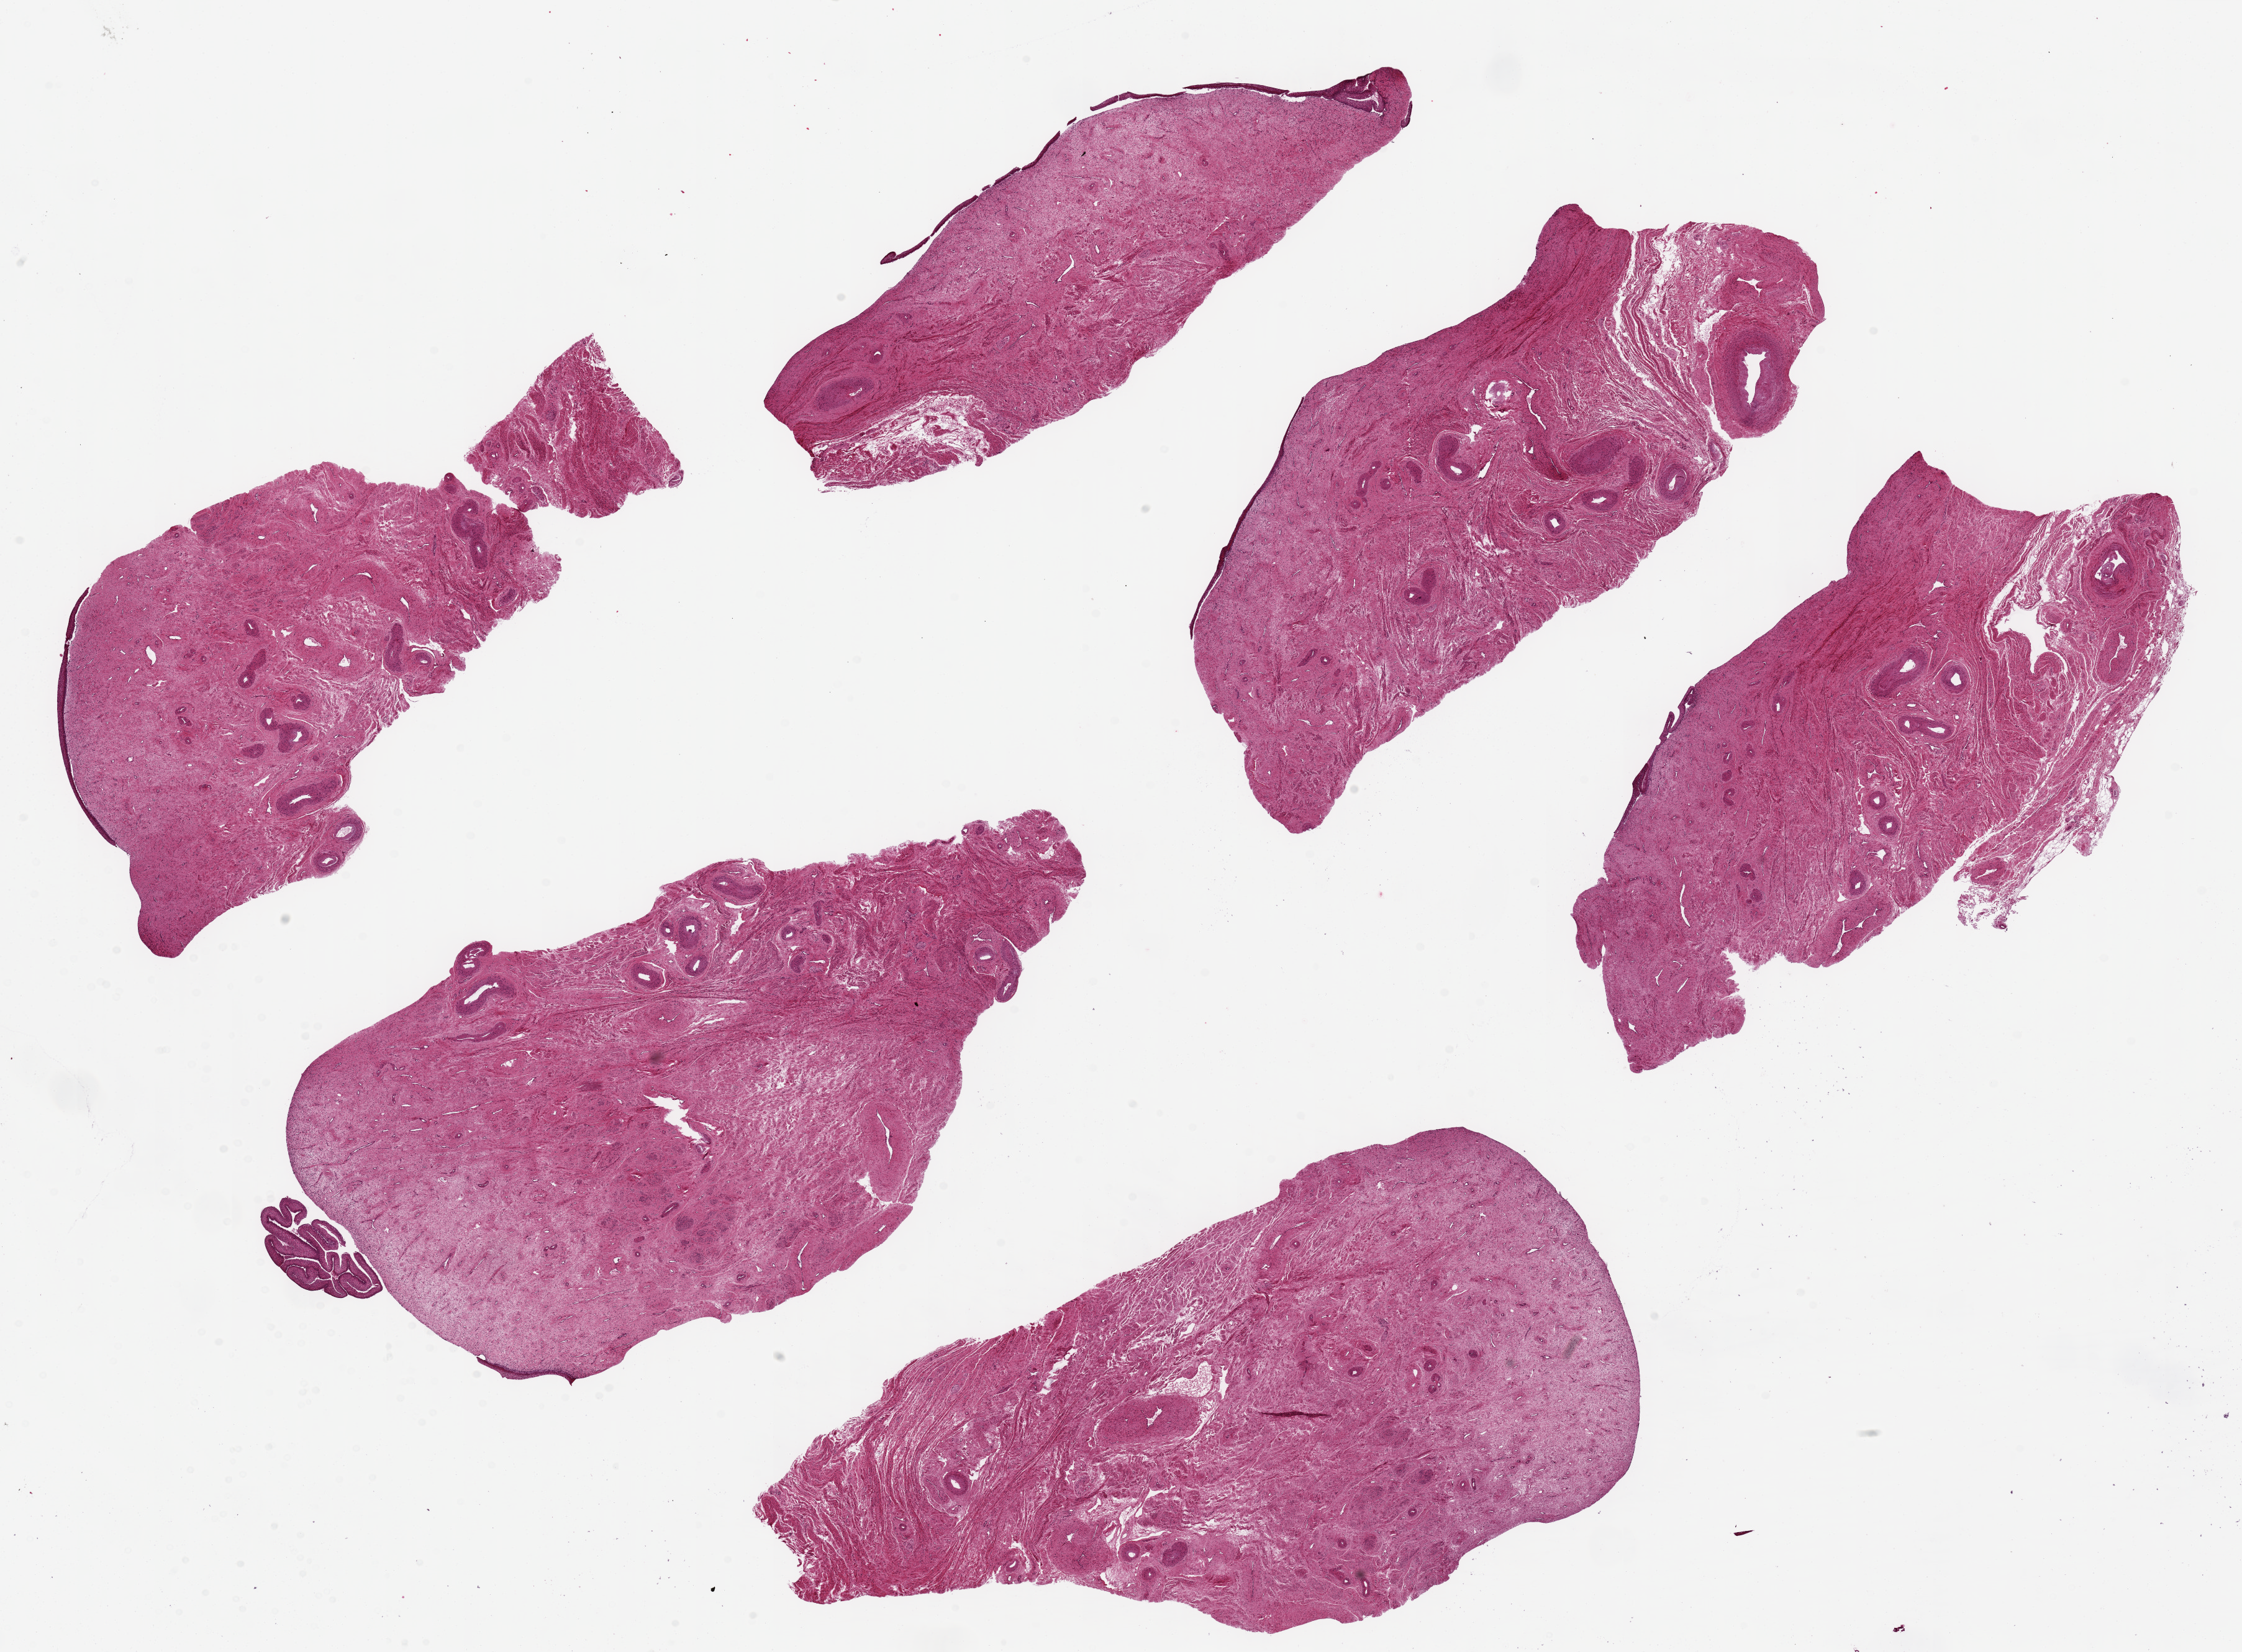
Haematoxylin and eosin whole-slide image — shown as a low-resolution overview of the whole scanned area (about 28.5 x 21.0 mm, acquisition: 20x scan). PAXgene-fixed, paraffin-embedded tissue. Target tissue: vagina. Donor tissue sample. Female donor.
Reviewer comment on this tissue sample: 6 pieces, up to 11x5.5 mm; atrophic epithelium.